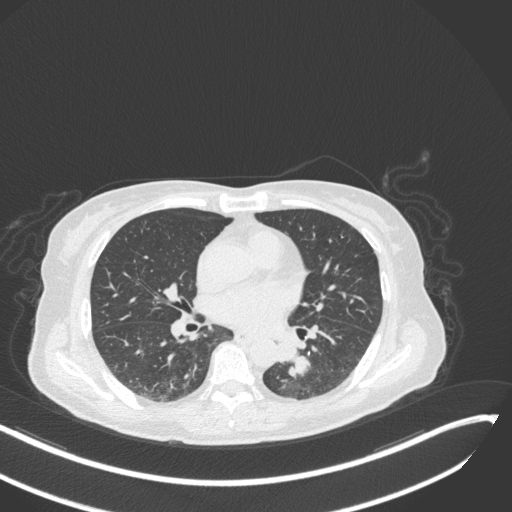
Chest CT, one axial slice; slice 130 of 342 in the series (ordered by position); reconstruction kernel B31f; 120 kVp; lung window (W 1500 / L -600 HU); 1 mm slice thickness; 512 × 512 image matrix, field of view 400 × 400 mm. Female patient, age 64 years. From the clinical record (not read from this slice): clinical TNM (as recorded): T3 N1 M1; histopathological grade: G3.
Outlined on this slice (bounding box drawn by a radiologist):
- lung tumour (recorded histology: small cell carcinoma): bounding box (x1, y1, x2, y2) in pixels: (273, 335, 315, 380)